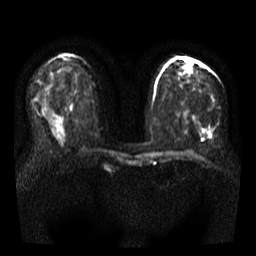
Breast MRI, one axial slice. Slice 19 of 35 in the series (ordered by position). Diffusion-weighted series; image 2 of 4 stored at this slice position (different b-values; order by instance number). 3 T. 5 mm slice thickness. 256 × 256 image matrix, field of view 320 × 320 mm. Female patient.
Annotated regions visible in this slice (manually delineated by an expert):
- tumour on diffusion-weighted imaging: bounding box <207,133,210,137> (left, top, right, bottom; pixels)